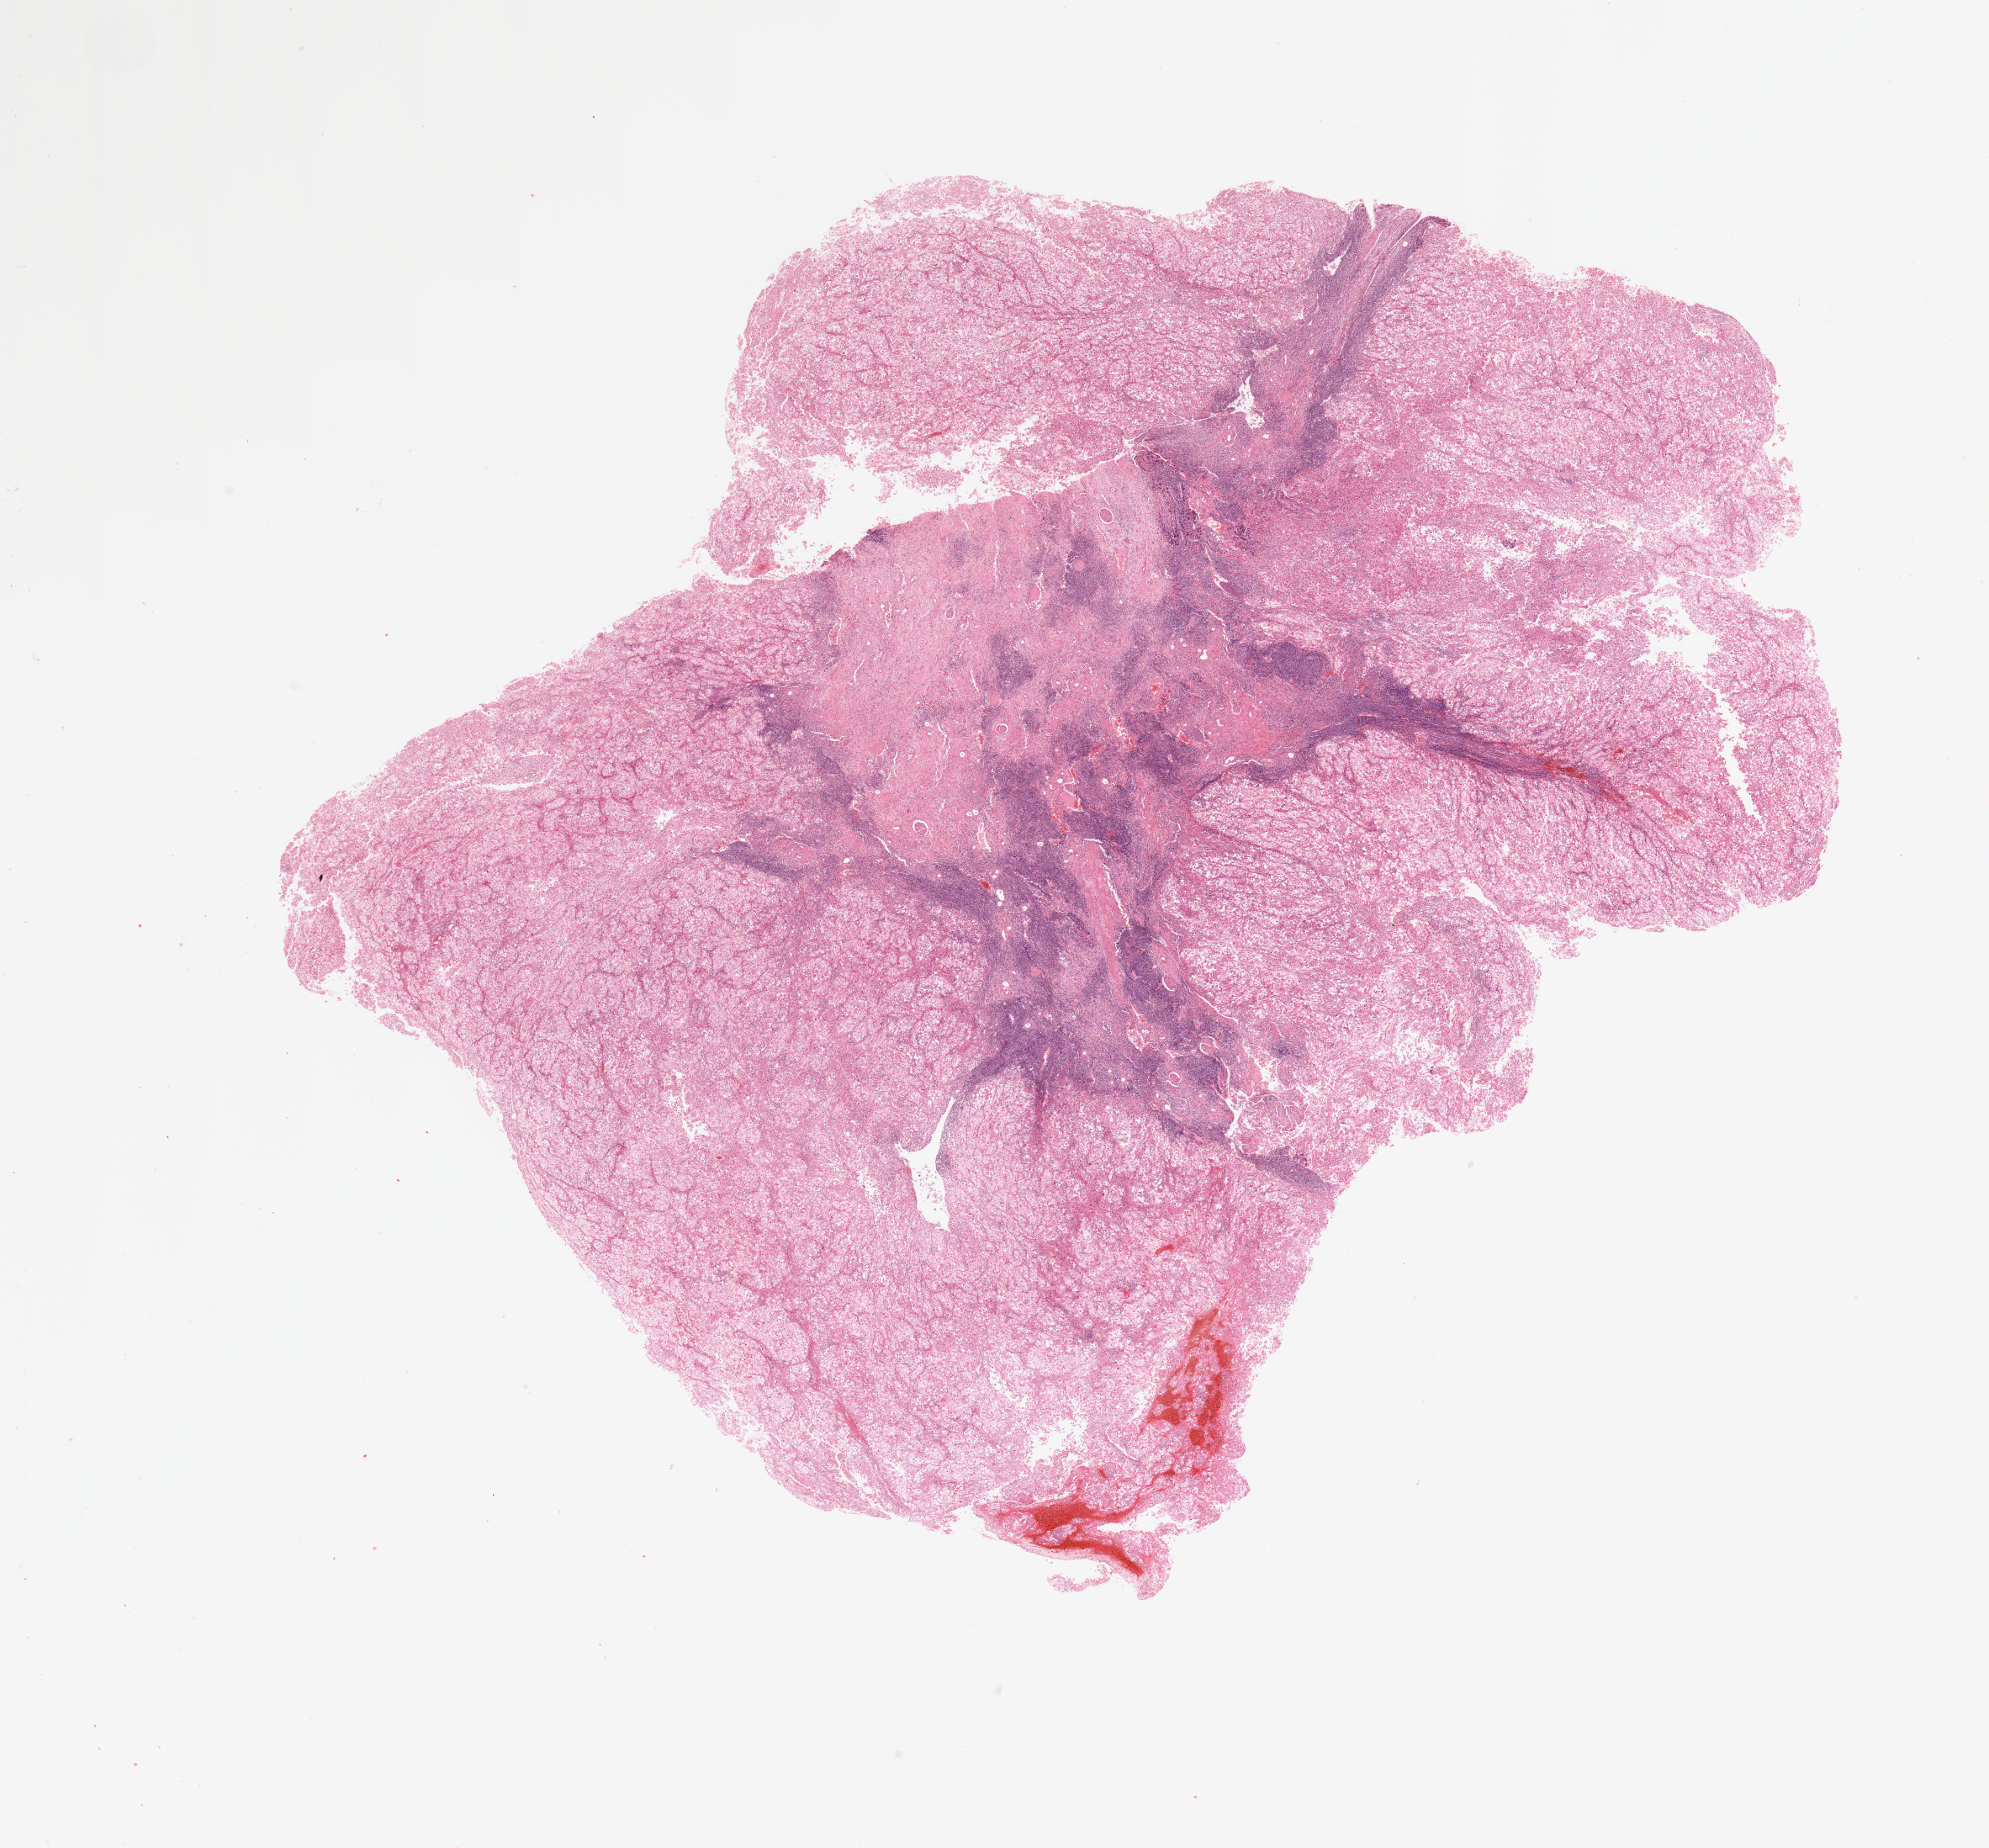
Hematoxylin and eosin (H&E) stained whole-slide image, a low-resolution overview of the entire scanned area, about 18.7 x 17.4 mm (acquisition: 20x scan). Tumour tissue sample, kidney. 68-year-old male patient. Histologic grade: G3 (poorly differentiated).
* AJCC pathologic stage: II
* diagnosis: Renal cell carcinoma, NOS